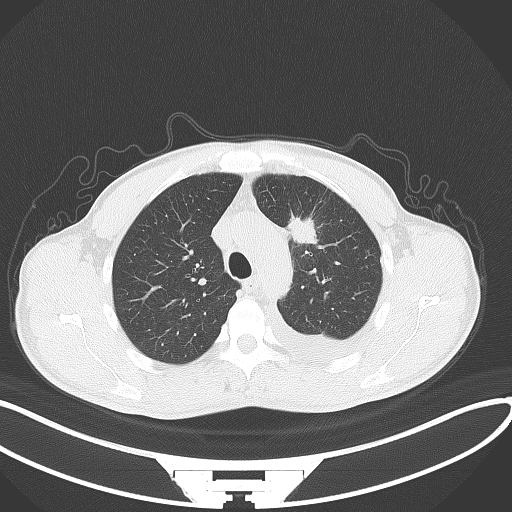
Chest CT, one axial slice; position 98 of 130 along the scan axis; reconstruction kernel B70f; 120 kVp; lung window (W 1500 / L -600 HU); 3 mm slice thickness; 512 × 512 image matrix, field of view 400 × 400 mm. Male patient, age 49 years. Case-level facts recorded for this patient, not image findings: clinical TNM (as recorded): T1c N1 M1.
Structures marked on this image (rectangle marked by the reading radiologist):
- lung tumour (recorded histology: adenocarcinoma): bounding box (x1, y1, x2, y2) in pixels: (287, 213, 323, 251)